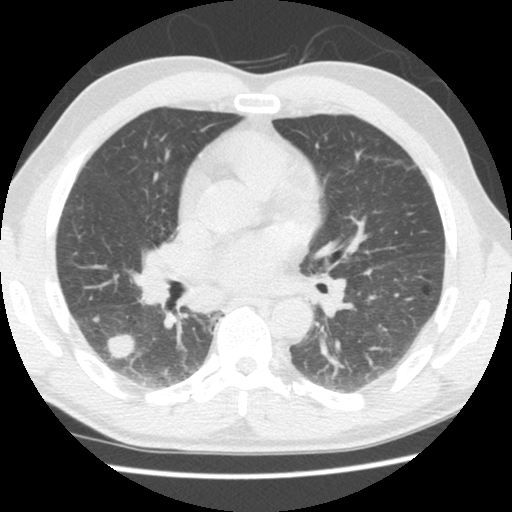
Axial slice from a low-dose chest CT screening exam. Second screening round (one year after baseline). Lung window (W 1500 / L -600 HU). 2.5 mm slice thickness. 140 kVp. Slice 78 of 133 in the series. 512 × 512 image matrix, field of view 320 × 320 mm. Male, age 60 years at enrolment. Former smoker at enrolment.
Expert reader's lesion annotation, bounding box <90,320,143,372> (left, top, right, bottom; pixels). Reader record for this screening exam (exam-level; its link to the box is not recorded): non-calcified nodule or mass ≥4 mm, right lower lobe, 17 × 15 mm, poorly defined margins, soft tissue attenuation, pre-existing on the prior screen: yes; interval growth: yes. Official screen result: positive, other. Later outcome: lung cancer diagnosed 44 days after this screen — adenocarcinoma, NOS, right lower lobe, stage IA (AJCC 6th edition), 18 mm at pathology.